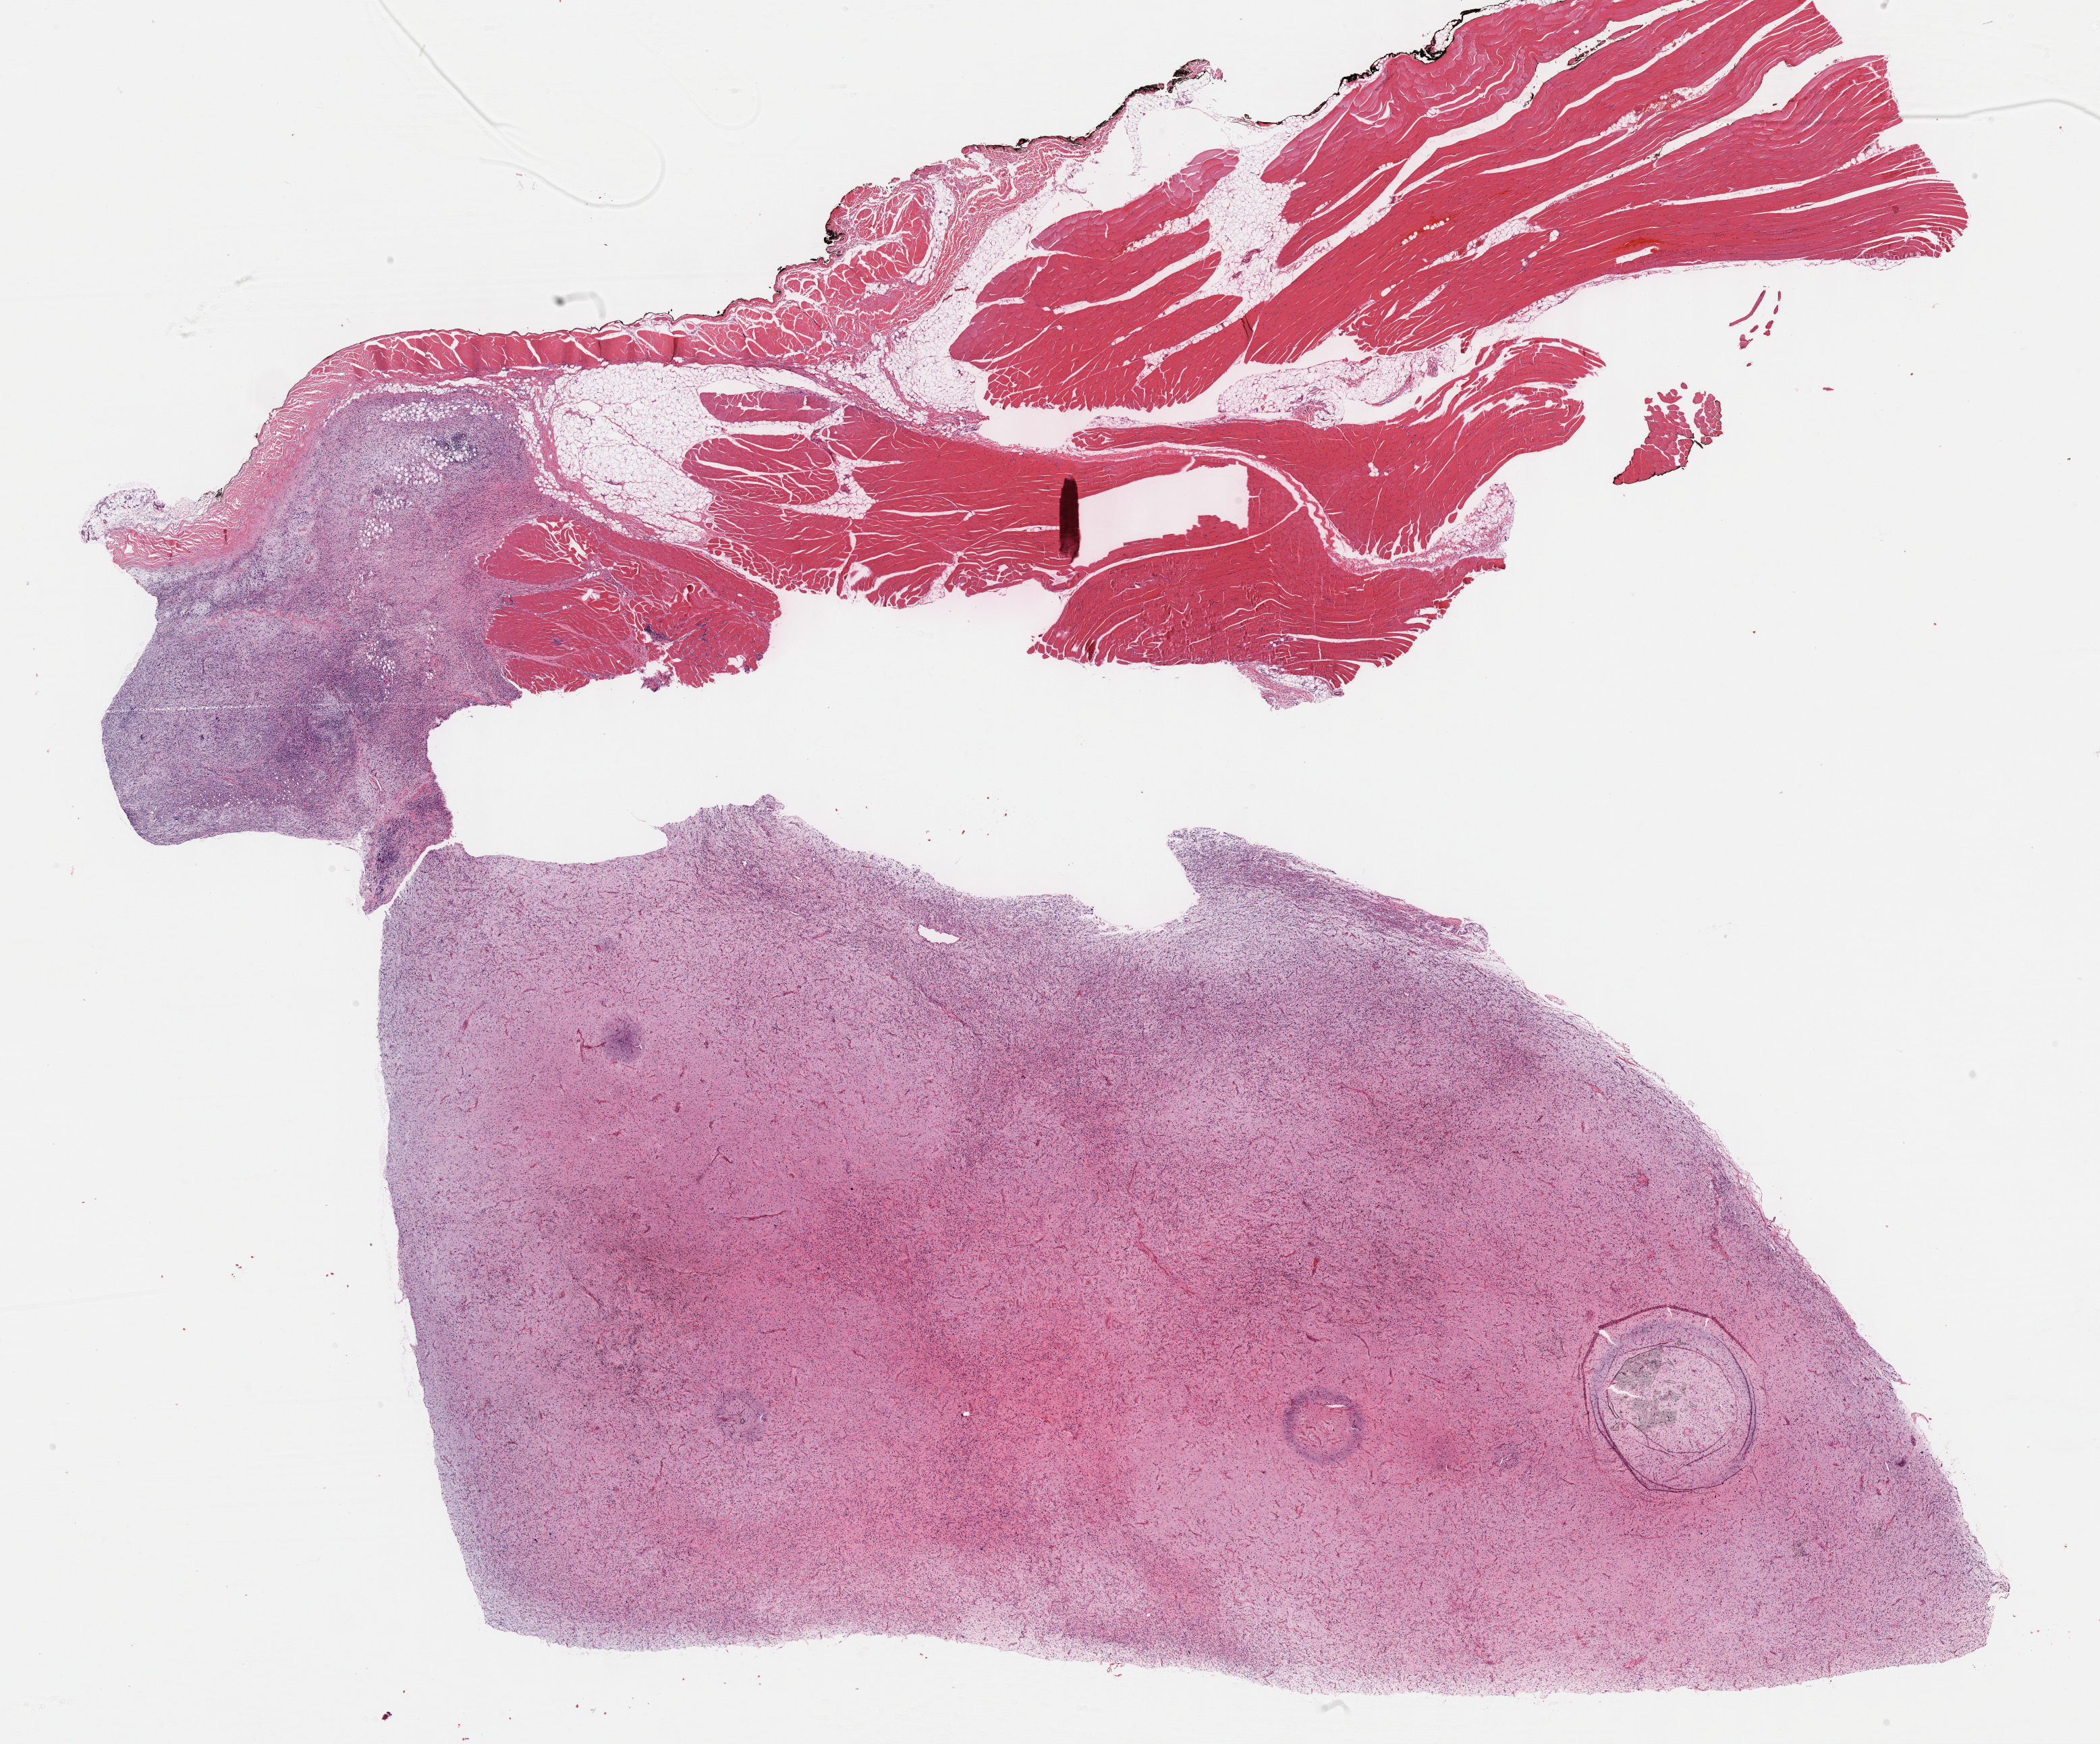
Whole-slide histology image, Hematoxylin and eosin (H&E) stained — whole scanned area (about 25.2 x 20.9 mm, acquisition: 40x scan) shown as a low-resolution overview. Formalin-fixed paraffin-embedded (FFPE) diagnostic section. Primary tumour sample from the connective, subcutaneous and other soft tissues. Male patient; age at initial diagnosis 35 years.
Diagnosis: Fibromyxosarcoma (connective, subcutaneous and other soft tissues of lower limb and hip).